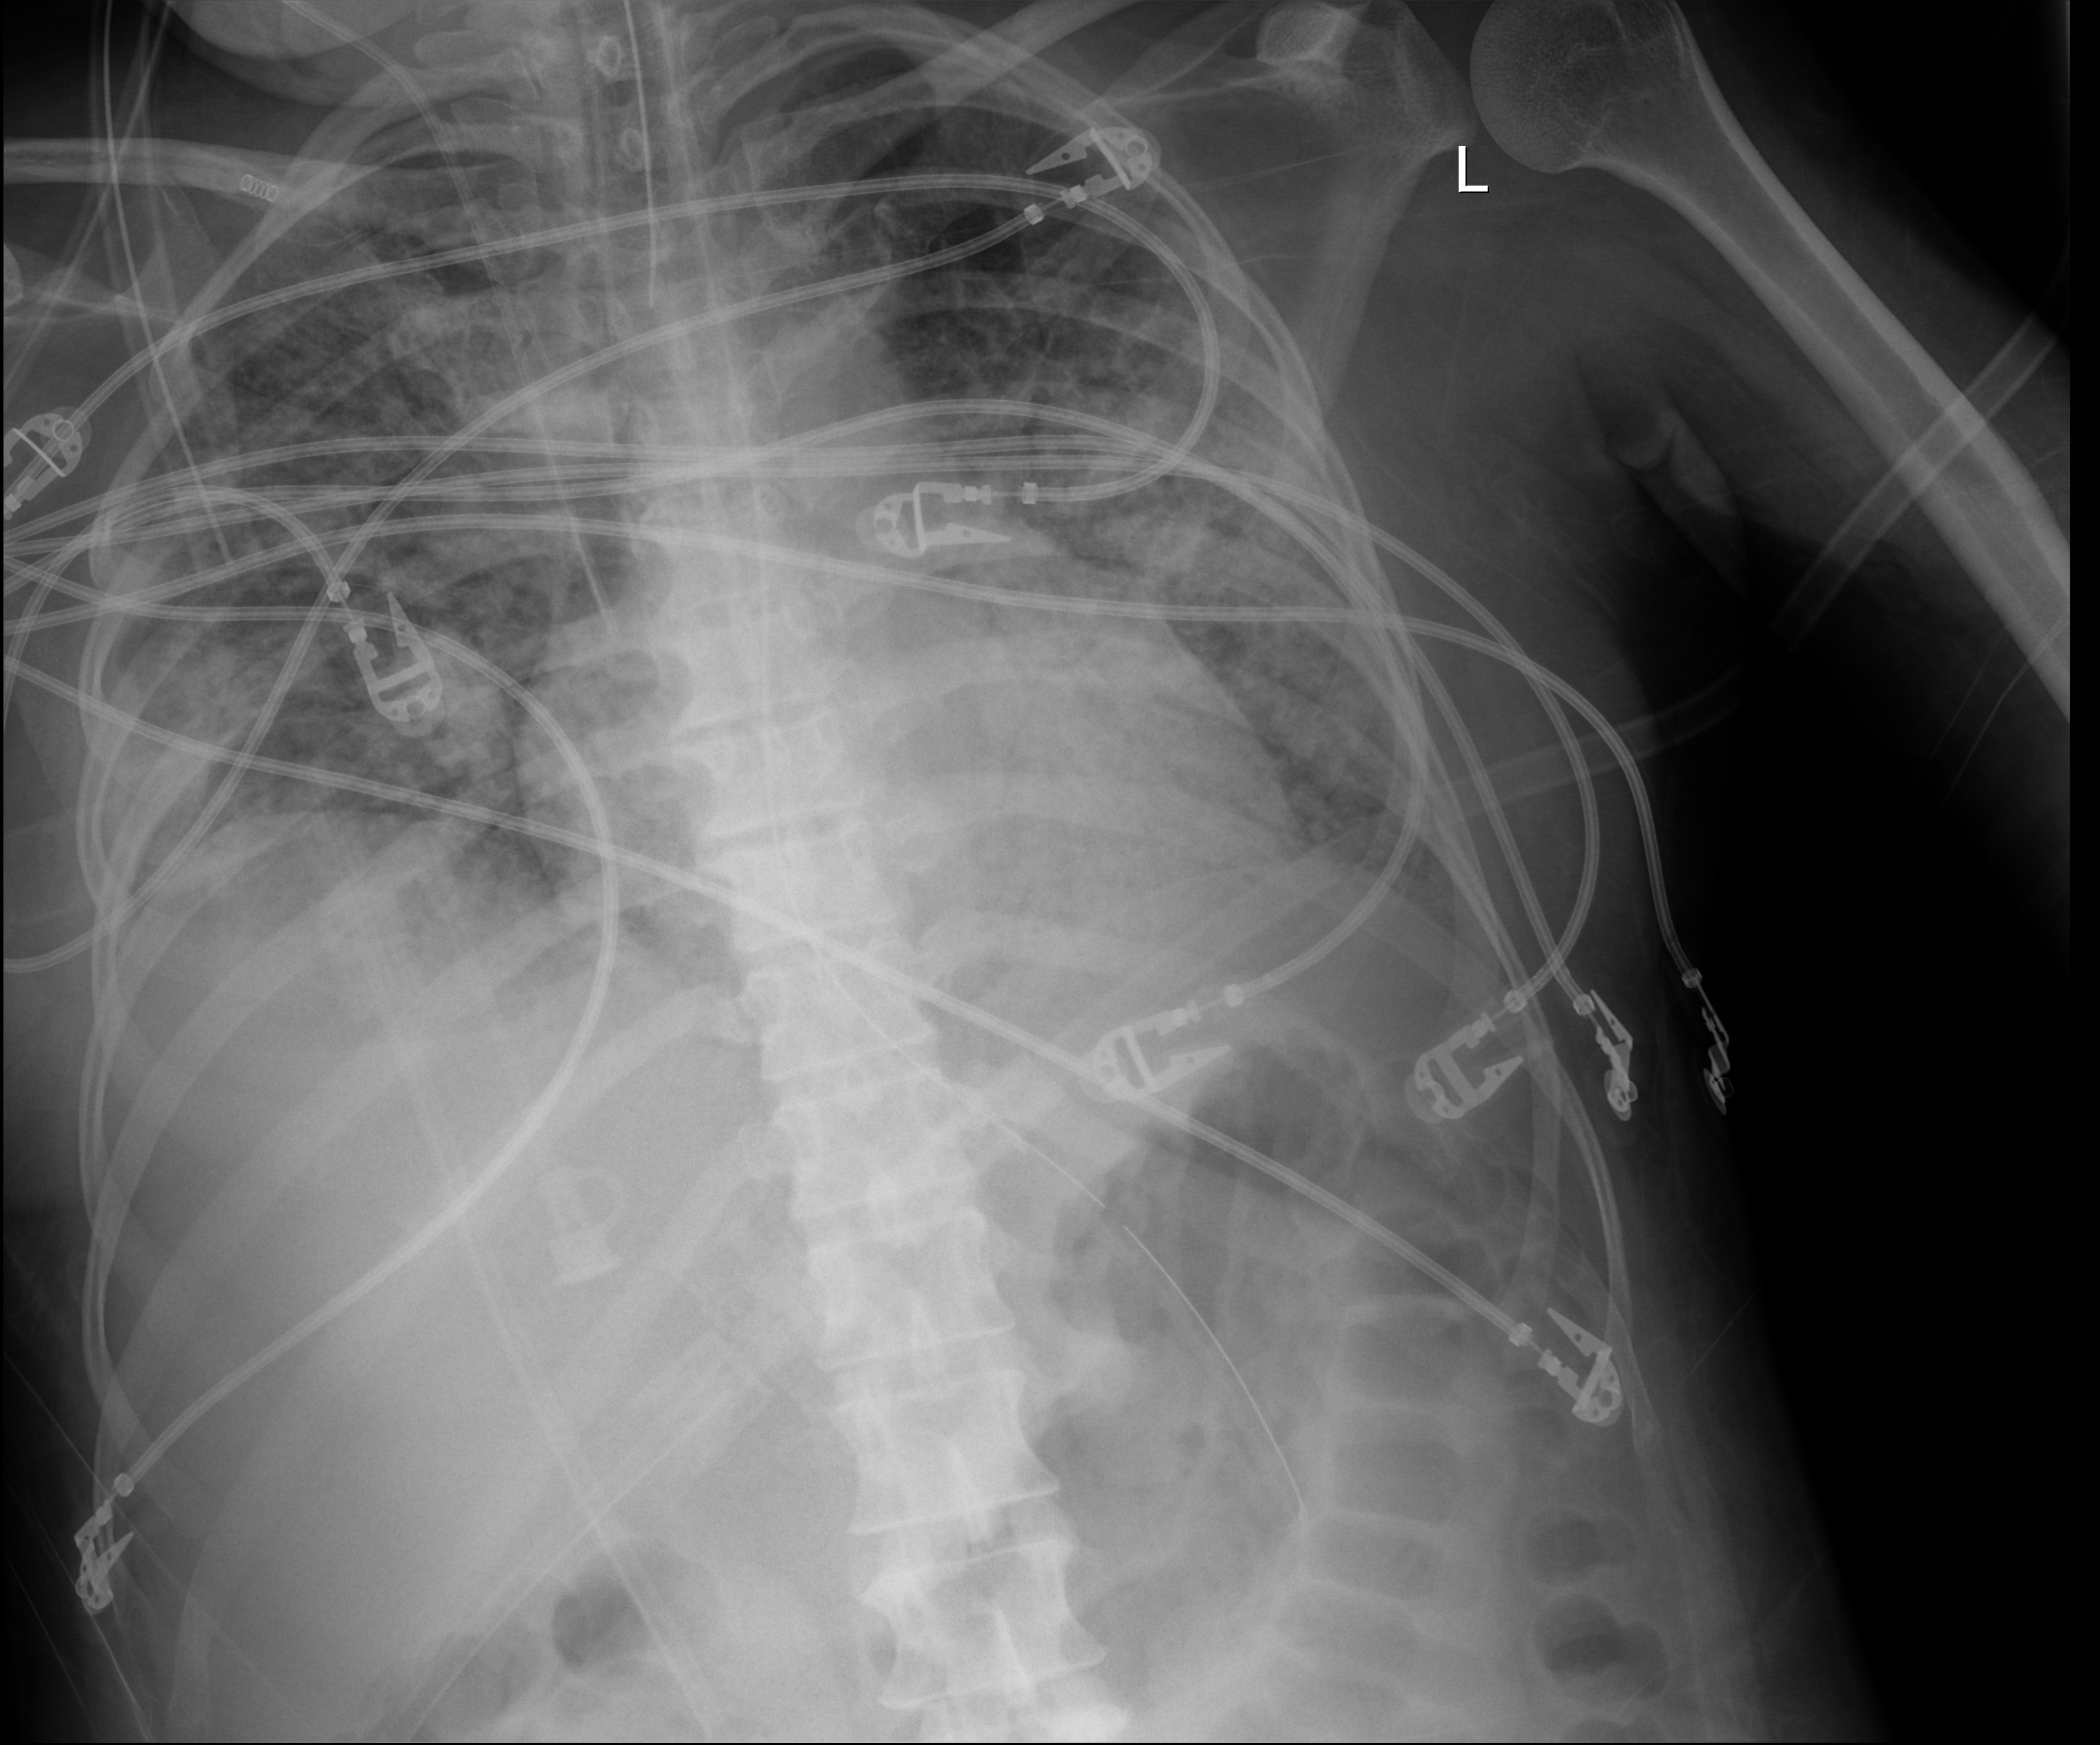
Portable chest radiograph, anteroposterior (AP) projection. Female patient hospitalised with COVID-19, age 18–59 years.
Hospital-stay facts (about this admission, not read from this image; timing relative to this image not recorded): length of hospital stay: 71 days.